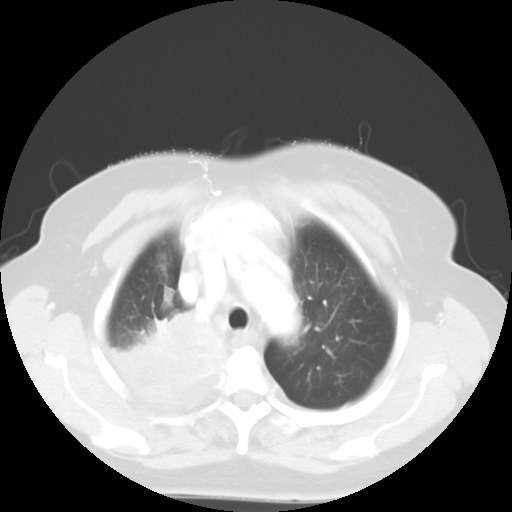
Chest CT, one axial slice; position 43 of 52 along the scan axis; 120 kVp; lung window (W 1500 / L -600 HU); 5 mm slice thickness; 512 × 512 image matrix. Female patient, age 81 years. Case-level facts recorded for this patient, not image findings: clinical TNM (as recorded): T4 N3 M1b.
Outlined on this slice (rectangle marked by the reading radiologist):
- lung tumour (recorded histology: adenocarcinoma): bounding box [x1, y1, x2, y2] px = [110, 306, 228, 411]